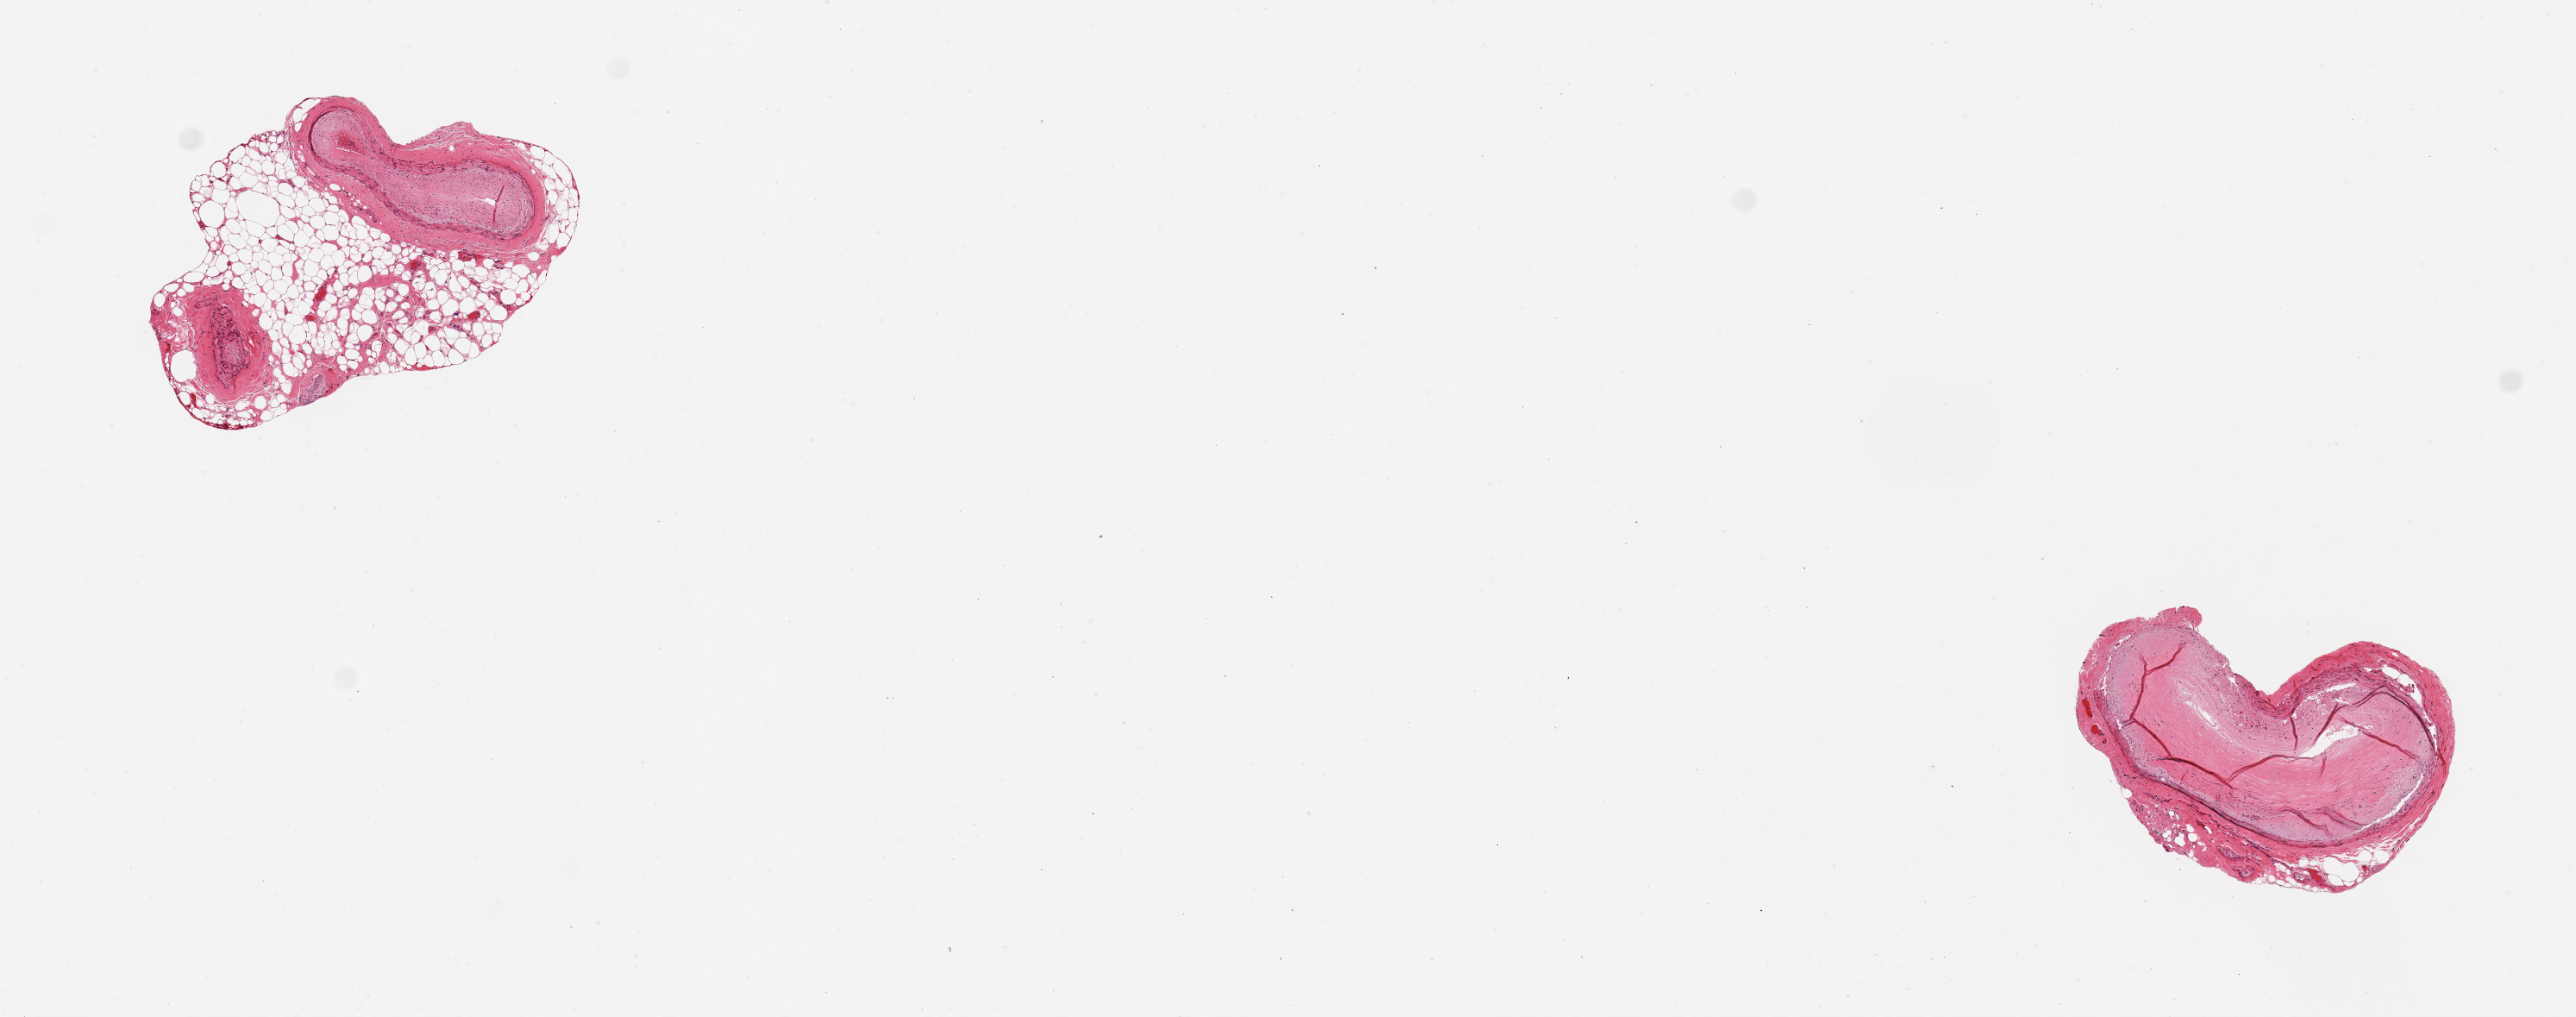
Whole-slide image, hematoxylin and eosin (H&E) stain — shown as a low-resolution overview of the whole scanned area (about 11.8 x 4.7 mm, from a 20x scan). PAXgene-fixed, paraffin-embedded tissue. Sampled site (target tissue): coronary artery. Tissue donor sample. Donor sex: male.
Review note (as recorded): 2 pieces, subtotoally occlusive atherosis; adherent nubbin of fat up to ~1.2 mm, section.